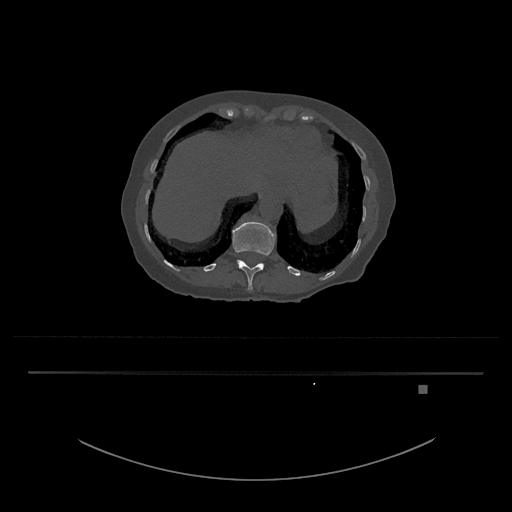
CT including the spine, one axial slice. Slice 604 of 797 in the series (ordered by position). 120 kVp. Bone window (W 1800 / L 400 HU). 0.5 mm slice thickness. 512 × 512 image matrix, field of view 500 × 500 mm. Female patient, age 57 years. From the clinical record (not read from this slice): primary cancer: cervical.
Outlined on this slice (semi-automatic segmentation, software-assisted and operator-edited):
- T12 vertebra: bounding box <232,221,276,290> (left, top, right, bottom; pixels)